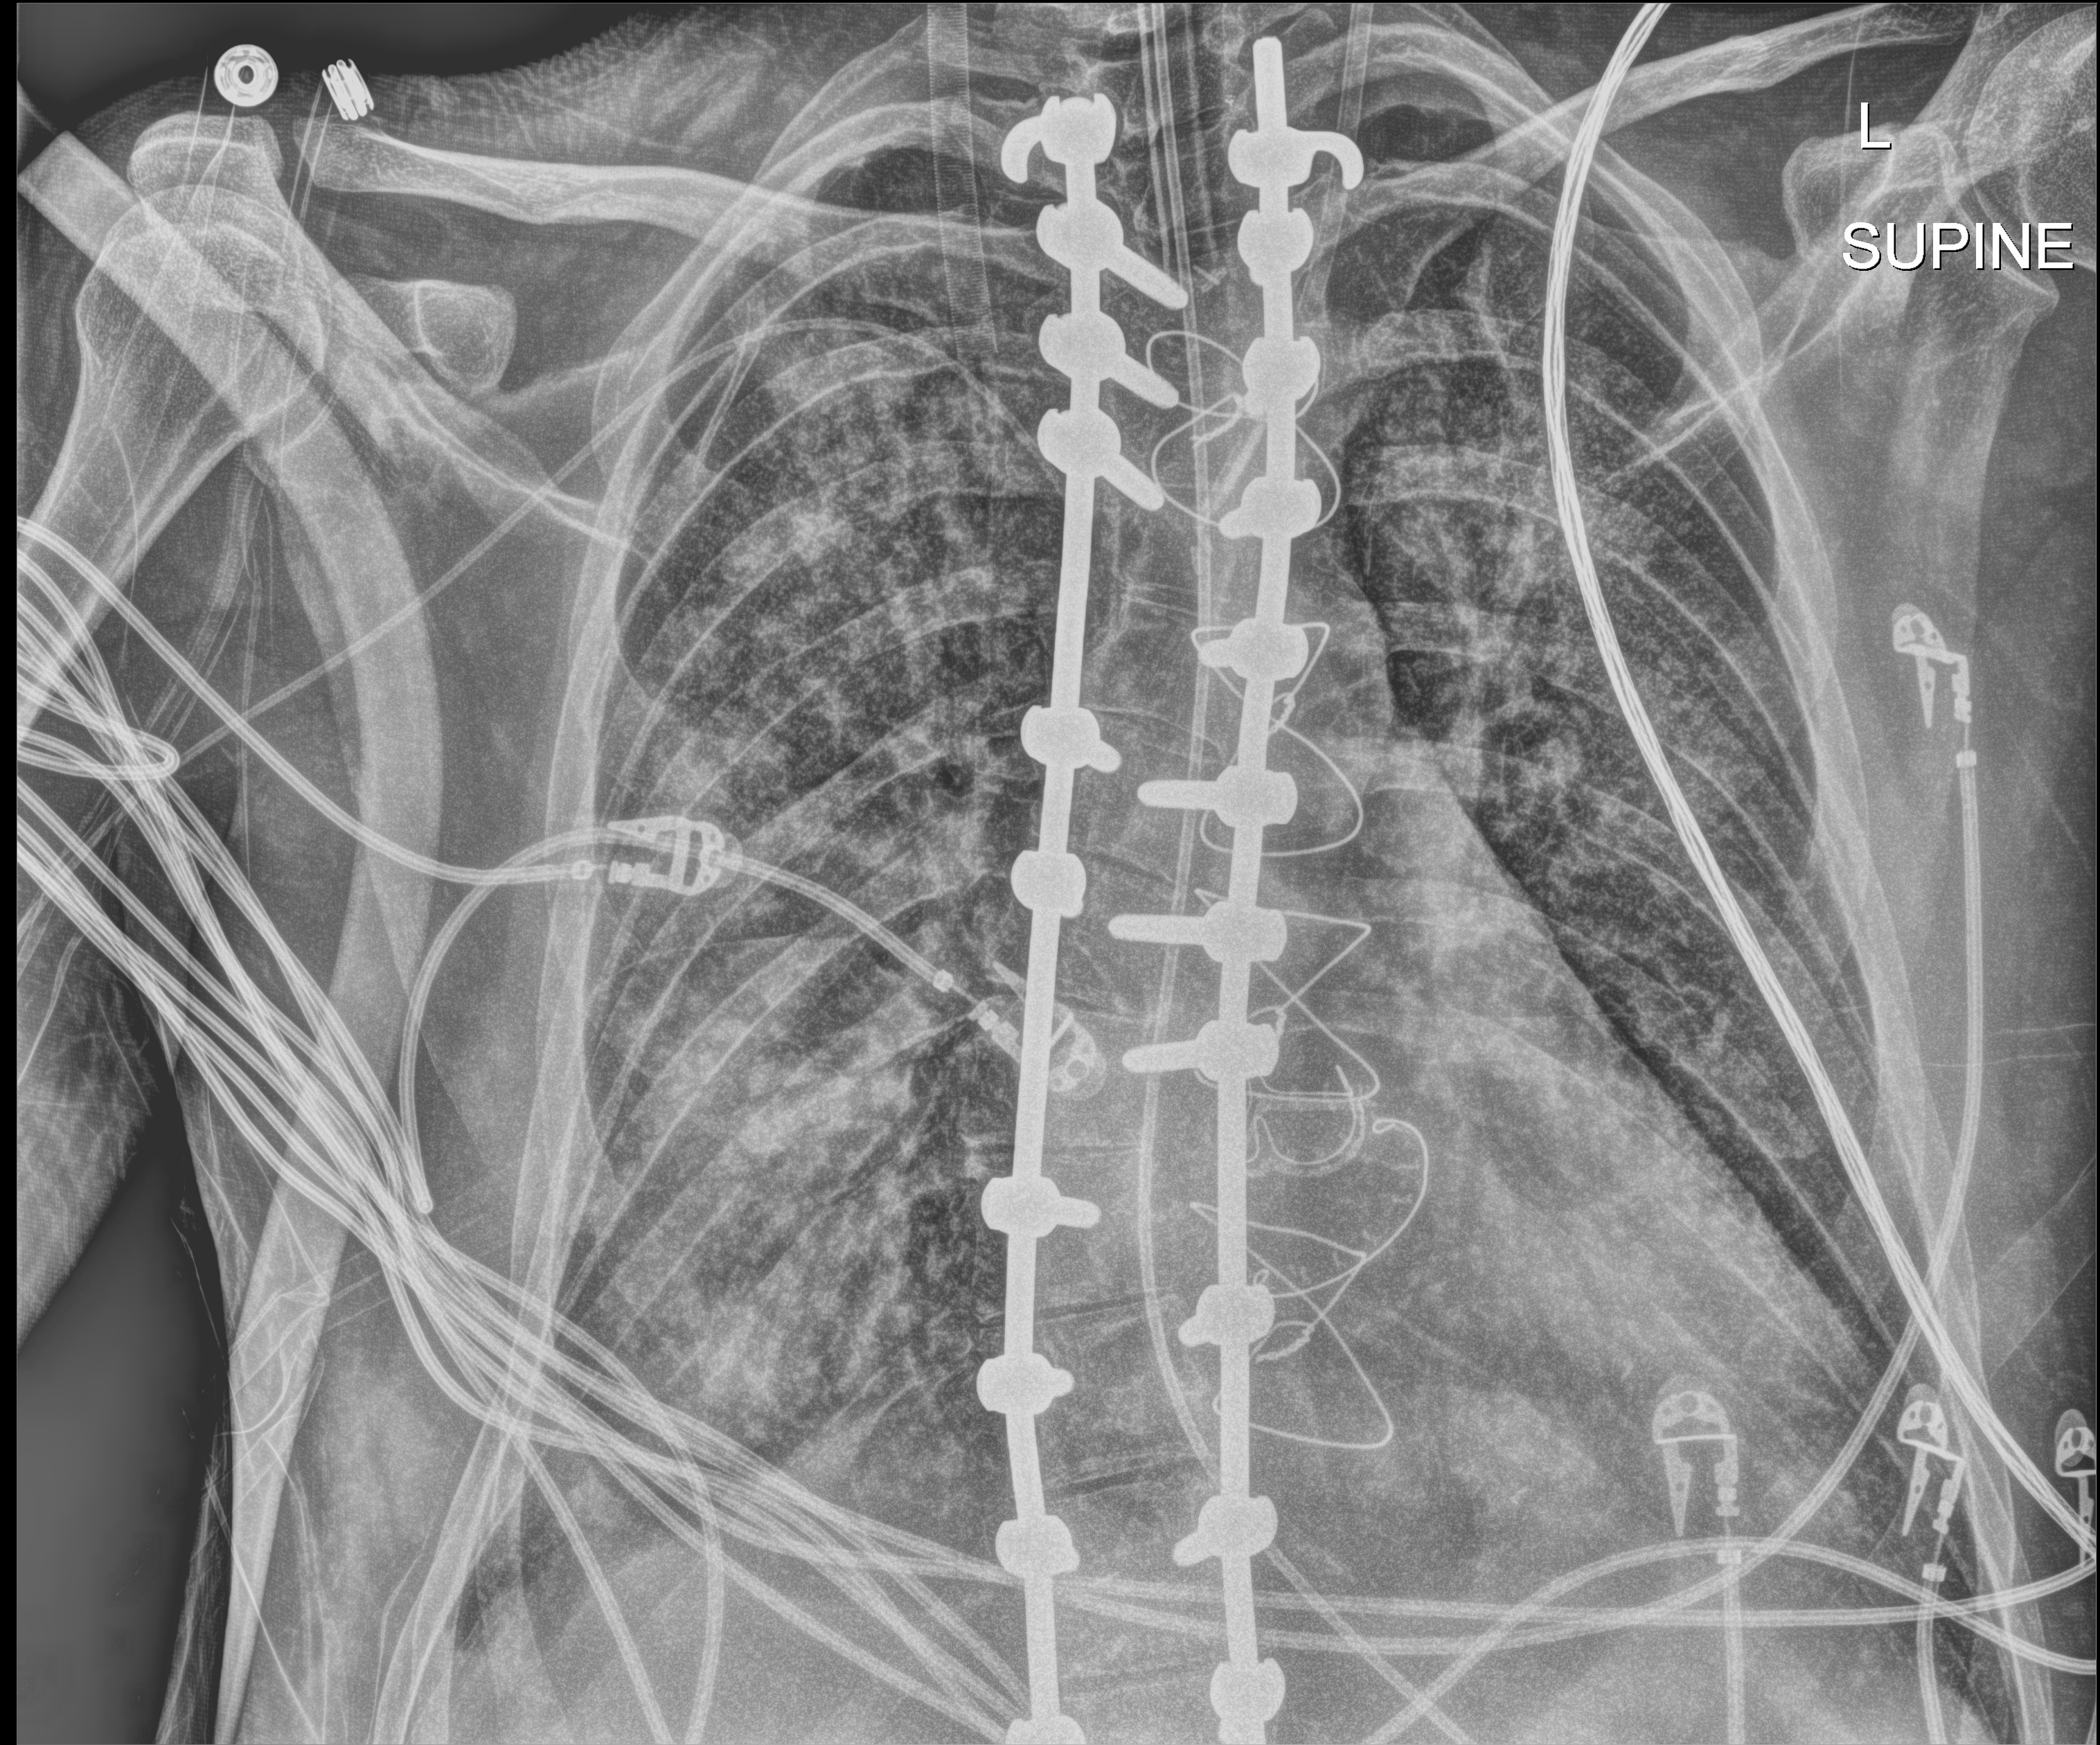
Bedside chest radiograph (digital radiography); anteroposterior (AP) projection. Patient hospitalised with COVID-19, aged 18–59 years.
Admission-level facts for this patient (not findings on this image; timing relative to this image not recorded): other chronic lung disease (admission record): no.